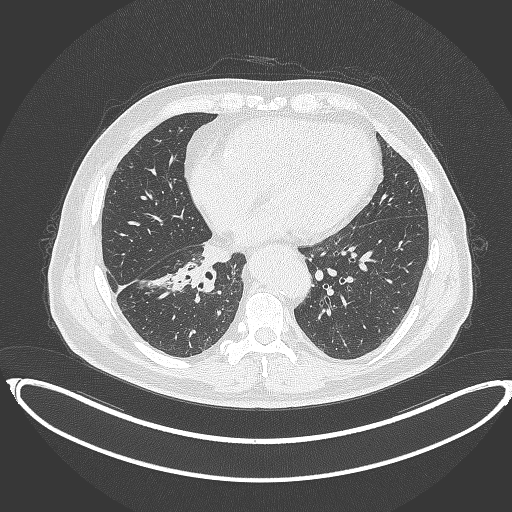
Chest CT, one axial slice; reconstruction kernel B70f; lung window (W 1500 / L -600 HU); 1 mm slice thickness; 512 × 512 image matrix, field of view 448 × 448 mm. Male patient, age 61 years. Case-level facts recorded for this patient, not image findings: clinical TNM (as recorded): T1b N1 M0.
Outlined on this slice (bounding box drawn by a radiologist):
- lung tumour (recorded histology: squamous cell carcinoma): bounding box [x1, y1, x2, y2] px = [170, 260, 216, 299]